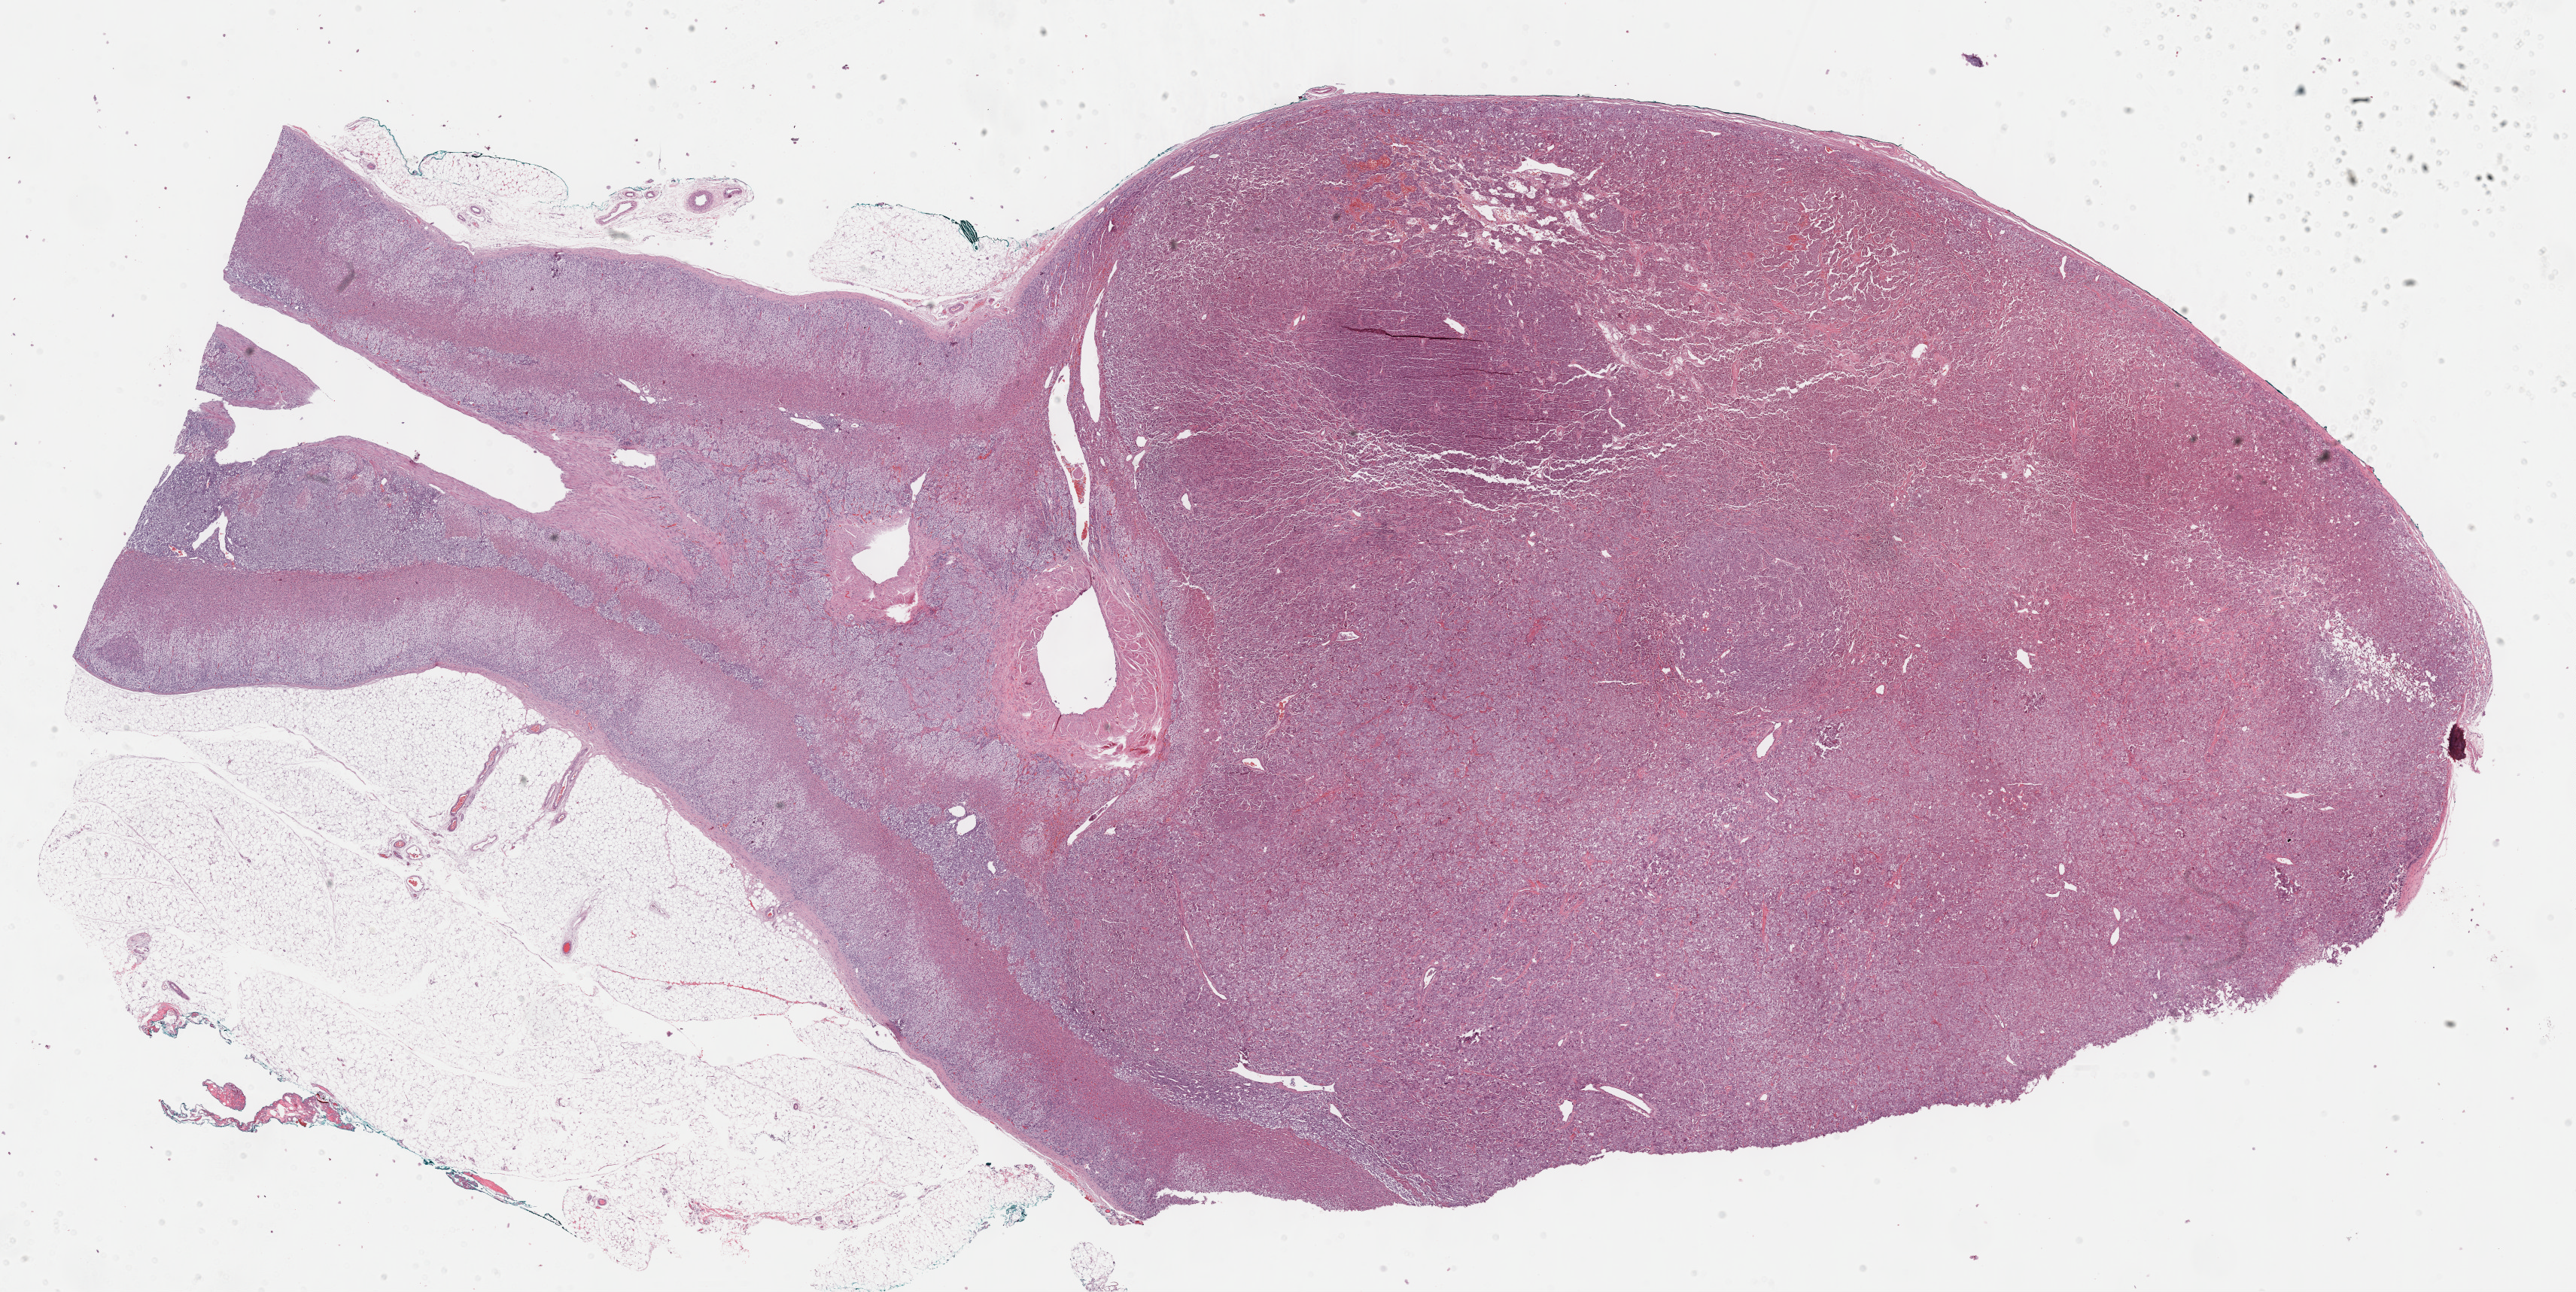
H&E-stained whole-slide image, shown as a low-resolution overview of the whole scanned area (about 27.7 x 13.9 mm). Formalin-fixed paraffin-embedded (FFPE) diagnostic section. Sample: primary tumour, adrenal gland. Female patient; age at initial diagnosis 46 years.
Histologic diagnosis: Pheochromocytoma, NOS.